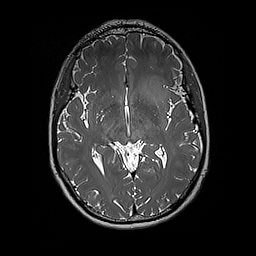
Brain MRI from a brain-tumour surgery series, one axial slice. Position 104 of 192 along the scan axis. 256 × 256 image matrix. From the clinical record (not read from this slice): histopathology: Glioblastoma; WHO grade: 4; IDH mutation: no.
Annotated regions visible in this slice (outlined manually by an expert reader):
- tumour: bounding box (x1, y1, x2, y2) in pixels: (140, 76, 171, 113)